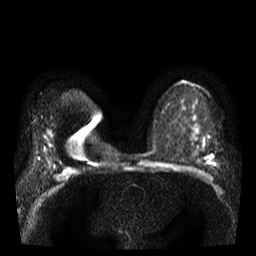
Breast MRI, one axial slice. Diffusion-weighted series; image 2 of 4 stored at this slice position (different b-values; order by instance number). 3 T. 5 mm slice thickness. 256 × 256 image matrix, field of view 320 × 320 mm. Female patient.
Structures marked on this image (manually delineated by an expert):
- tumour on diffusion-weighted imaging: bounding box [x1, y1, x2, y2] px = [212, 155, 214, 158]